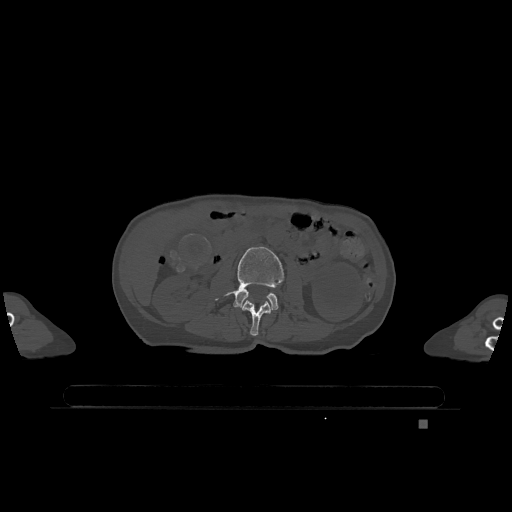
CT including the spine, one axial slice; position 381 of 1317 along the scan axis; bone window (W 1800 / L 400 HU); 0.5 mm slice thickness; 512 × 512 image matrix, field of view 500 × 500 mm. Female patient, age 74 years. From the clinical record (not read from this slice): primary cancer: lung.
Structures marked on this image (semi-automatically segmented with operator editing):
- L2 vertebra: box from (x=242, y=300) to (x=271, y=336) px
- L3 vertebra: (x=216, y=247)–(x=285, y=310)